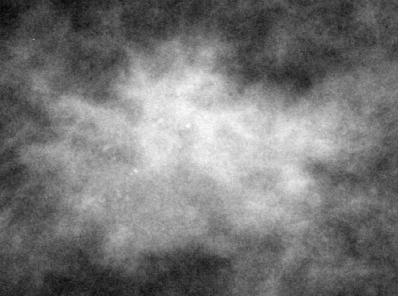
Crop from a digitized film mammogram around one marked abnormality; right breast; CC view; BI-RADS breast density category 1 (scale 1–4).
Finding: mass, shape irregular, margins spiculated; BI-RADS assessment category 5; subtlety rating 5 on a 1 (subtle) to 5 (obvious) scale; pathology (as recorded): malignant.